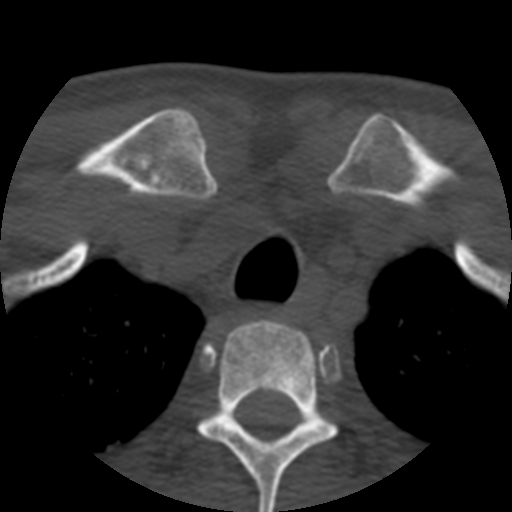
CT including the spine, one axial slice. Position 430 of 508 along the scan axis. Reconstruction kernel STANDARD. 120 kVp. Bone window (W 1800 / L 400 HU). 1.25 mm slice thickness. 512 × 512 image matrix, field of view 160 × 160 mm. Patient age 57 years. From the clinical record (not read from this slice): primary cancer: prostate.
Outlined on this slice (semi-automatically segmented with operator editing):
- T2 vertebra: bounding box [x1, y1, x2, y2] px = [197, 321, 337, 512]
- T3 vertebra: [327, 419, 331, 423]